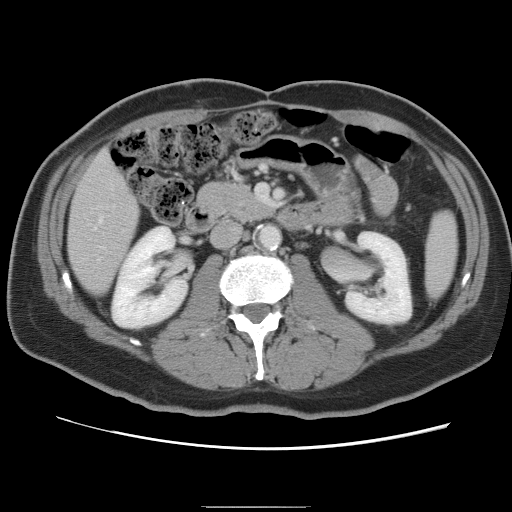
Contrast-enhanced abdominal CT, one axial slice; position 29 of 87 along the scan axis; intravenous contrast given; soft-tissue window (W 400 / L 40 HU); 5 mm slice thickness; 512 × 512 image matrix, field of view 363 × 363 mm. Male patient, age 63 years. From the clinical record (not read from this slice): diagnosis: colorectal cancer liver metastases, imaged before liver resection; multiple liver metastases: no; largest metastasis: 9 cm; chemotherapy before resection: no.
Outlined on this slice (outlined manually by an expert reader):
- hepatic veins: box from (x=95, y=218) to (x=101, y=229) px
- liver: (x=69, y=153)–(x=139, y=294)
- planned liver remnant (the part of the liver to remain after resection): (x=69, y=152)–(x=139, y=294)